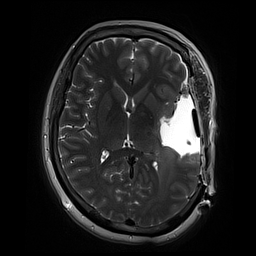
Brain MRI from a brain-tumour surgery series, one axial slice. Position 39 of 70 along the scan axis. 256 × 256 image matrix. From the clinical record (not read from this slice): histopathology: Glioblastoma; WHO grade: 4; IDH mutation: no; tumour location: Left Temporal.
Annotated regions visible in this slice (manually delineated by an expert):
- residual tumour: box from (x=159, y=106) to (x=175, y=139) px